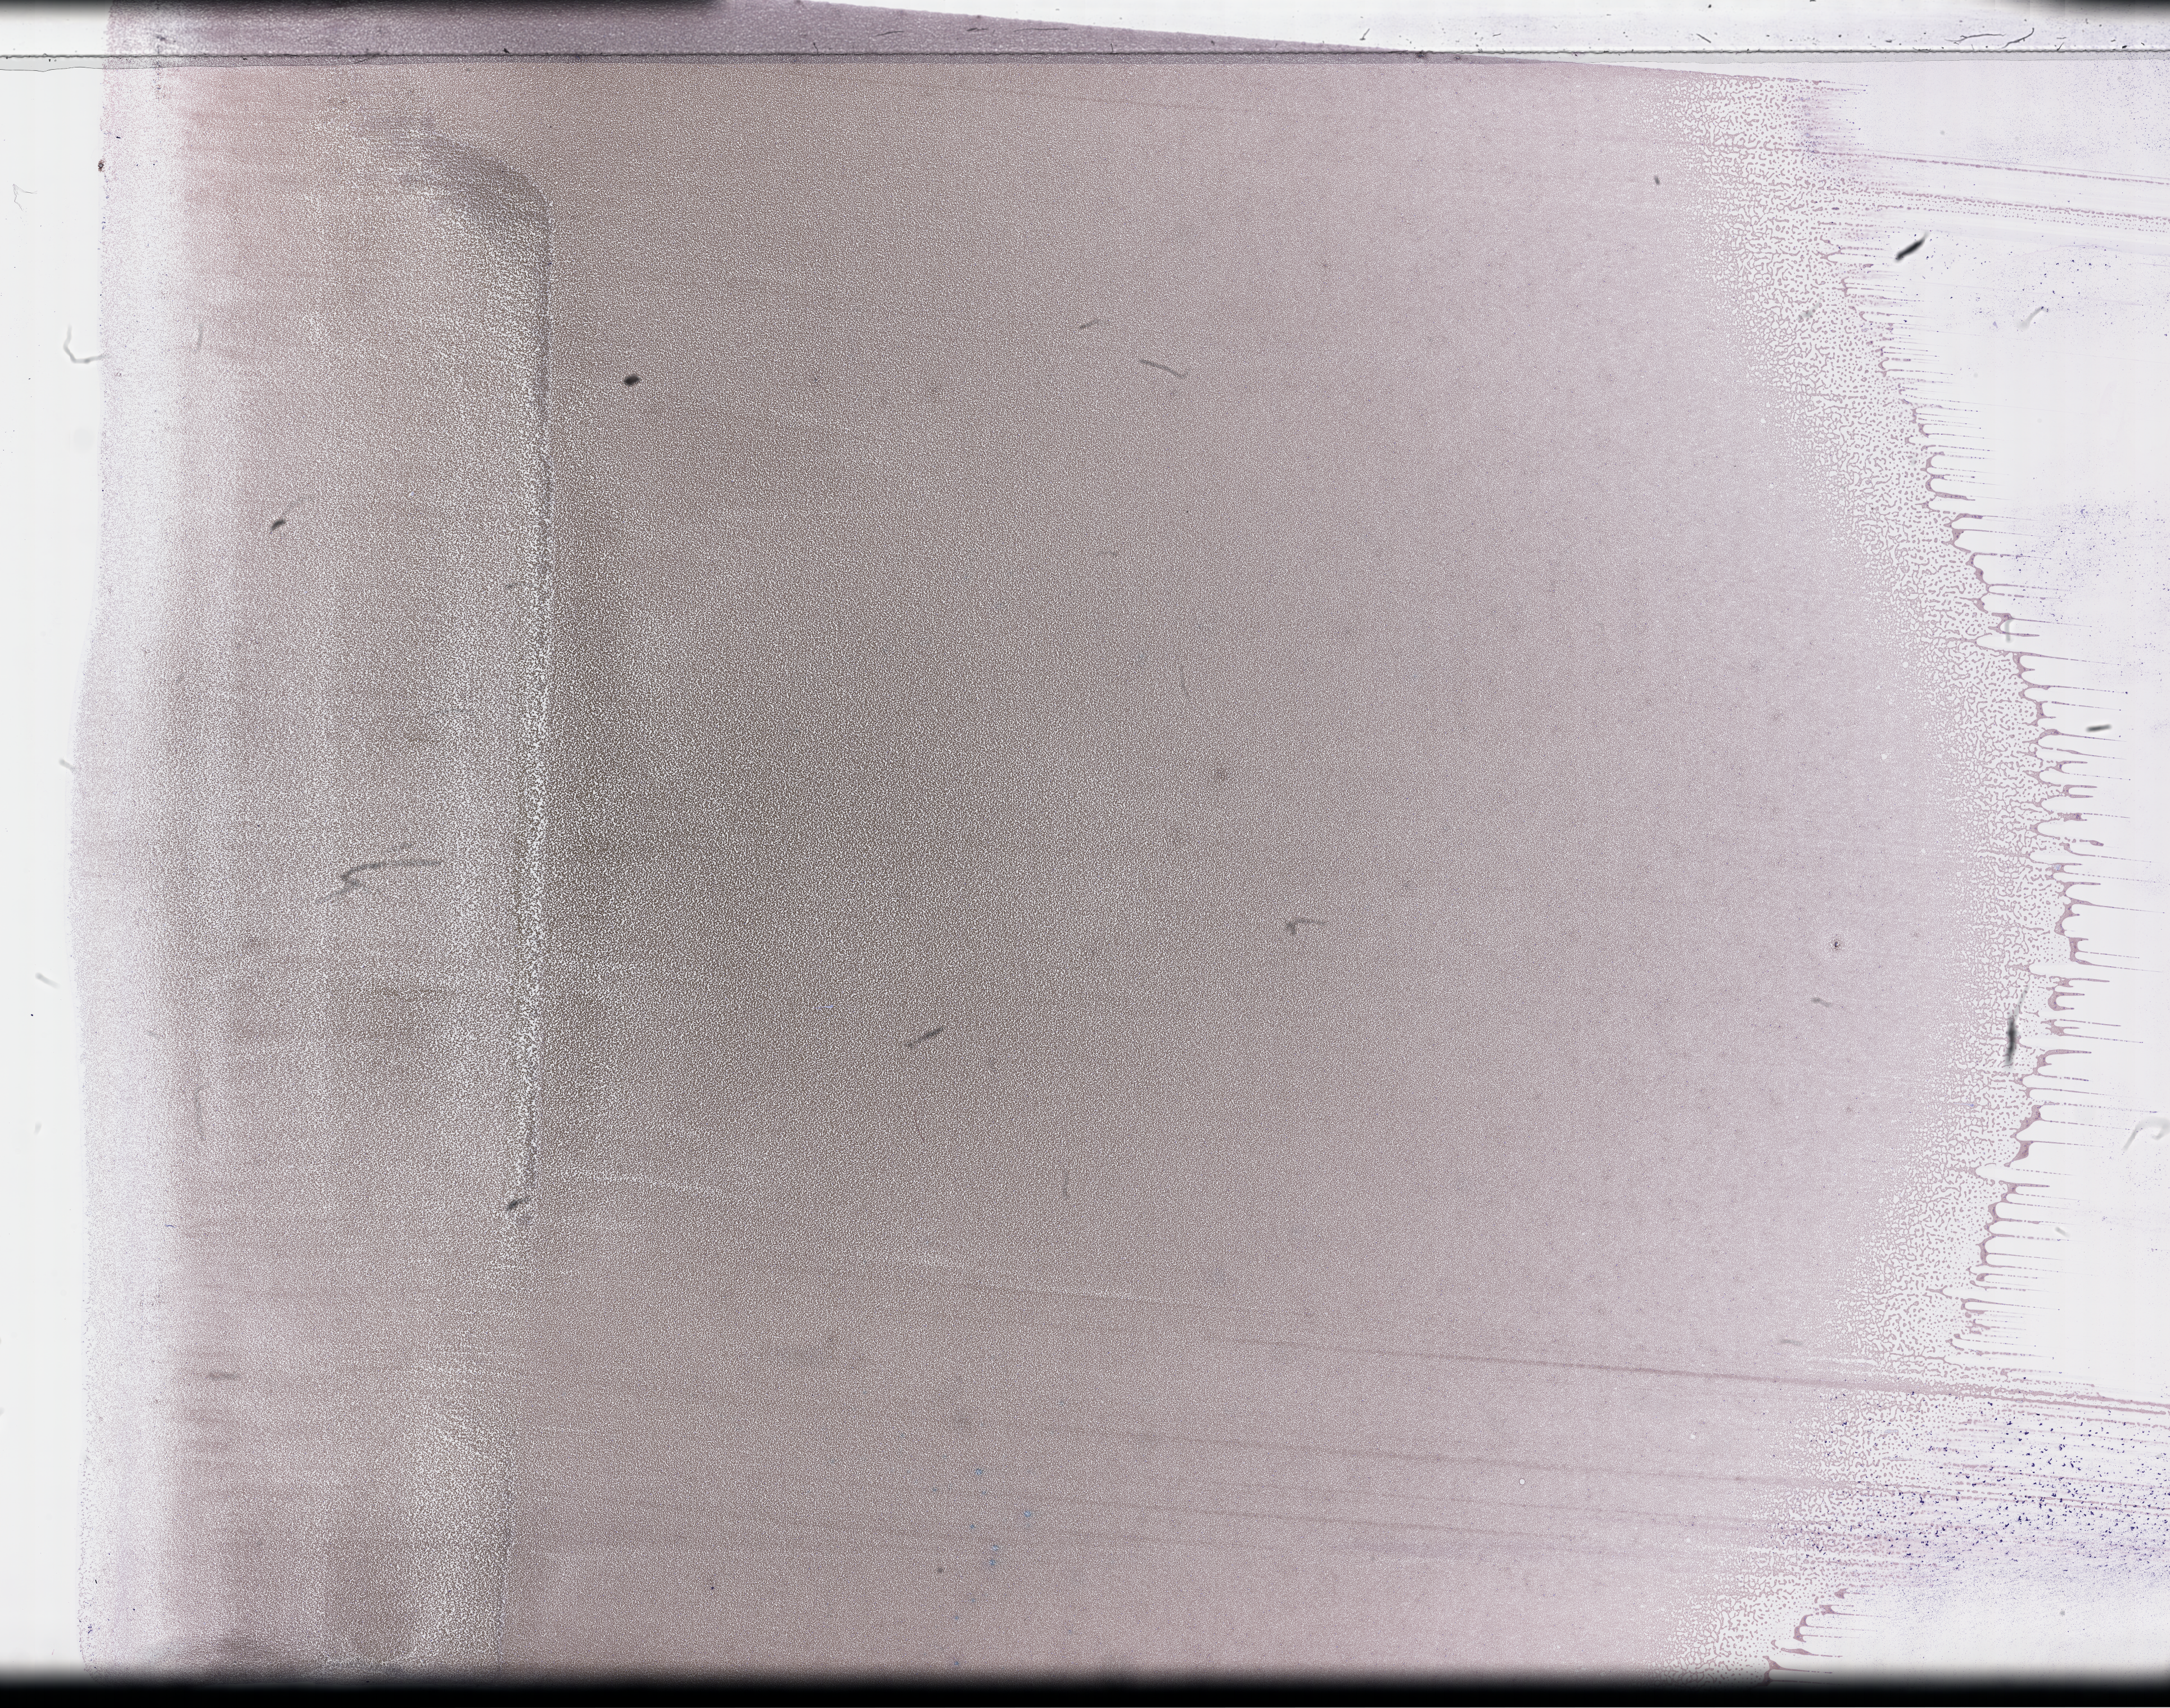
Whole-slide image of a whole blood smear, Wright-Giemsa stain — low-resolution overview of the scanned area, about 31.2 x 24.5 mm. EDTA-anticoagulated smear. Collected on treatment. Patient: male.
Patient diagnosis: Plasma Cell Myeloma.